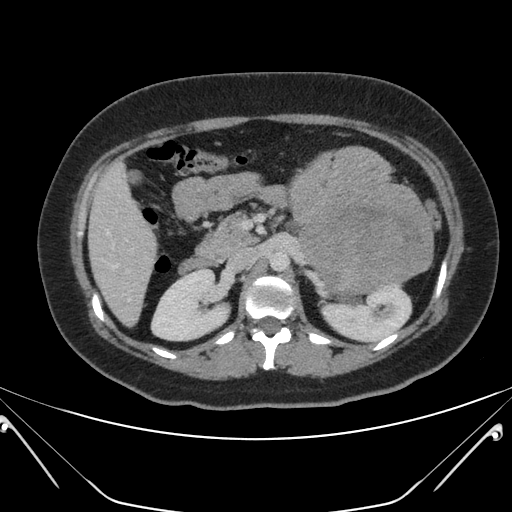
Contrast-enhanced abdominal CT, one axial slice; slice 117 of 168 in the series (ordered by position); soft-tissue window (W 400 / L 40 HU); 3 mm slice thickness; 512 × 512 image matrix. Patient: female, 26 years. Case-level facts recorded for this patient, not image findings: diagnosis: adrenocortical carcinoma; tumour side: left adrenal; tumour size at pathology: 28 cm; Ki-67 index: 20 %; stage (as recorded): 2.
Structures marked on this image (semi-automatic segmentation, software-assisted and operator-edited):
- mass: bounding box [x1, y1, x2, y2] px = [289, 144, 437, 293]